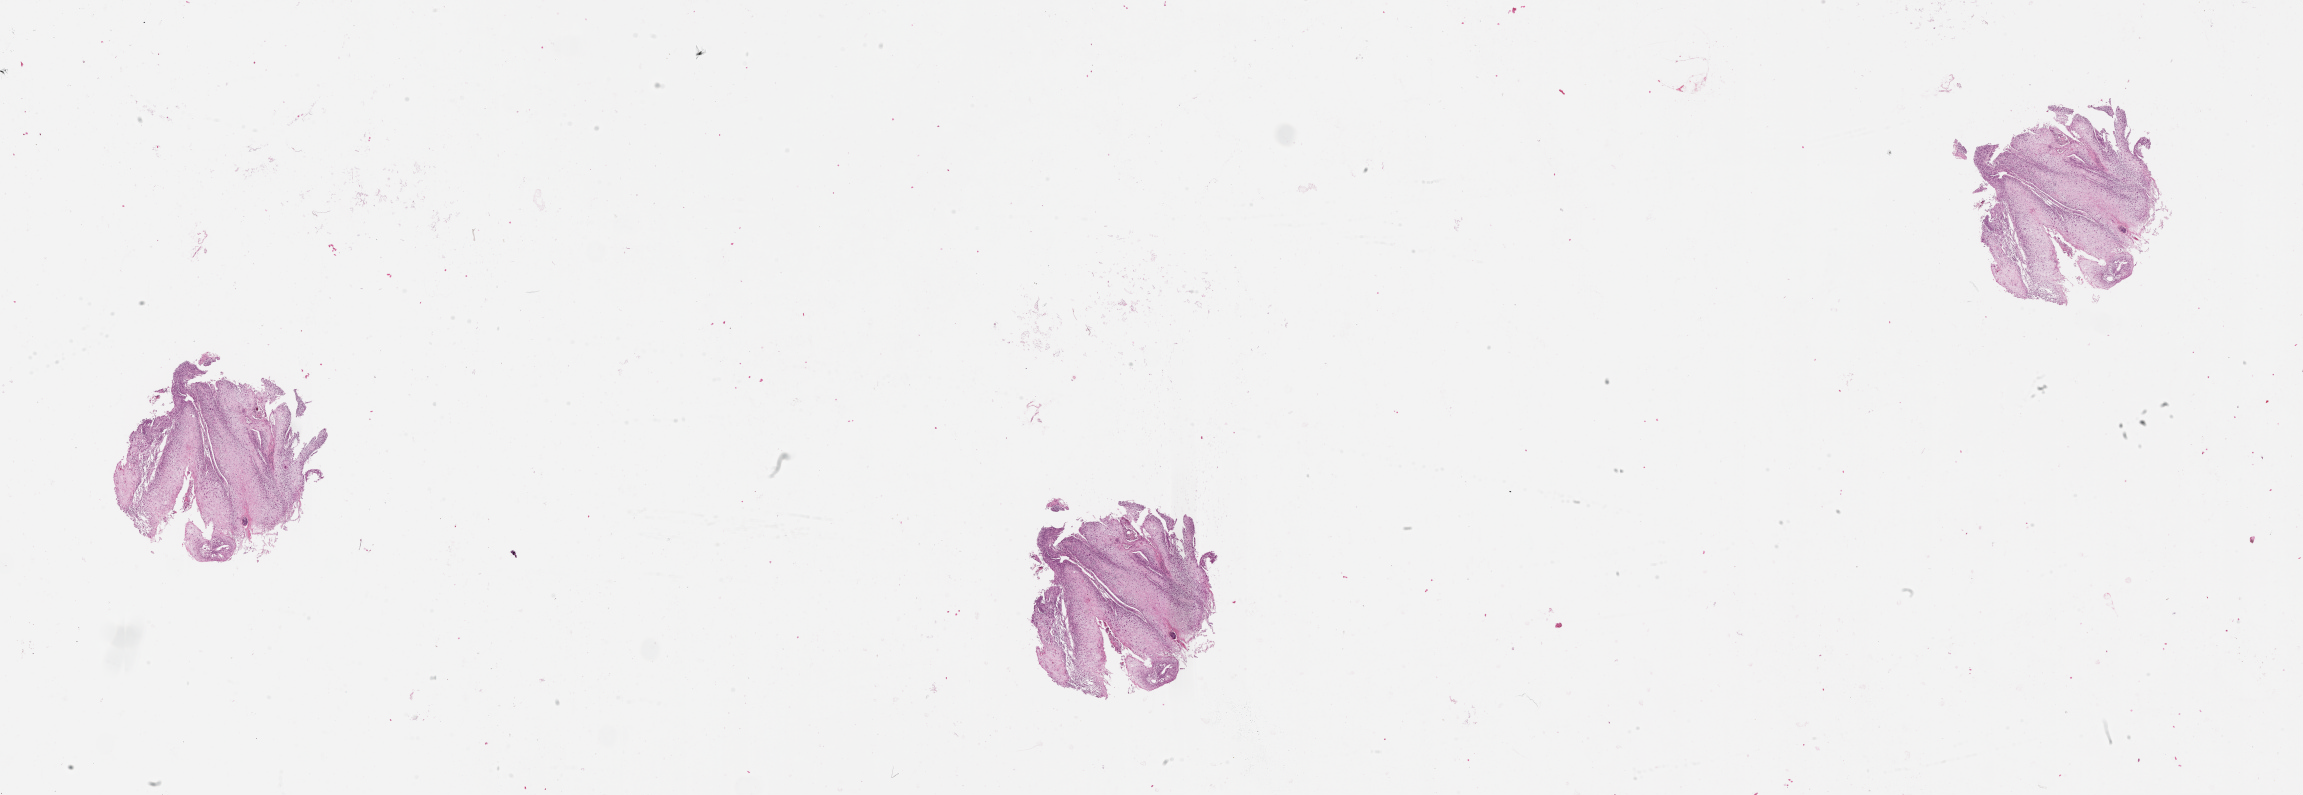
Digitized H&E tissue section (whole slide) — whole scanned area (about 37.1 x 12.8 mm) shown as a low-resolution overview, tumour tissue sample, sampled site: floor of mouth. Patient: male, age 70 years. Histologic grade: G1 (well differentiated). Pathologist review of this section (percent, as recorded): tumour nuclei 85%, necrosis 5%.
• AJCC pathologic stage: II
• primary tumour site (as recorded): oral cavity
• histologic diagnosis: Squamous cell carcinoma, NOS (floor of mouth, NOS)